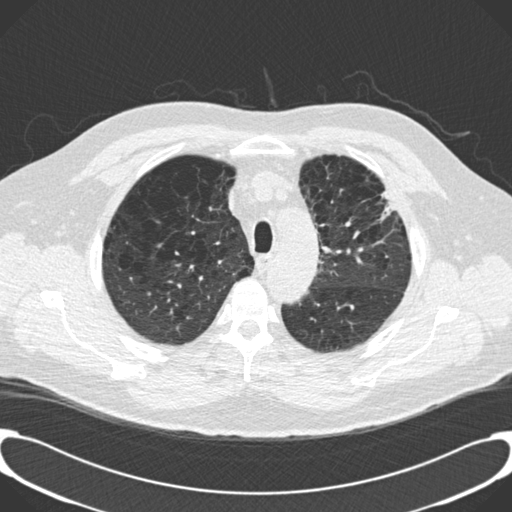
Low-dose screening chest CT, one axial slice; slice 156 of 189 in the series (ordered by position); reconstruction kernel B30f; lung window (W 1500 / L -600 HU); 512 × 512 image matrix, field of view 380 × 380 mm.
Outlined on this slice (outlined manually by an expert reader):
- lesion 1 (tumor, upper lobe of left lung): bounding box (x1, y1, x2, y2) in pixels: (381, 190, 396, 220)